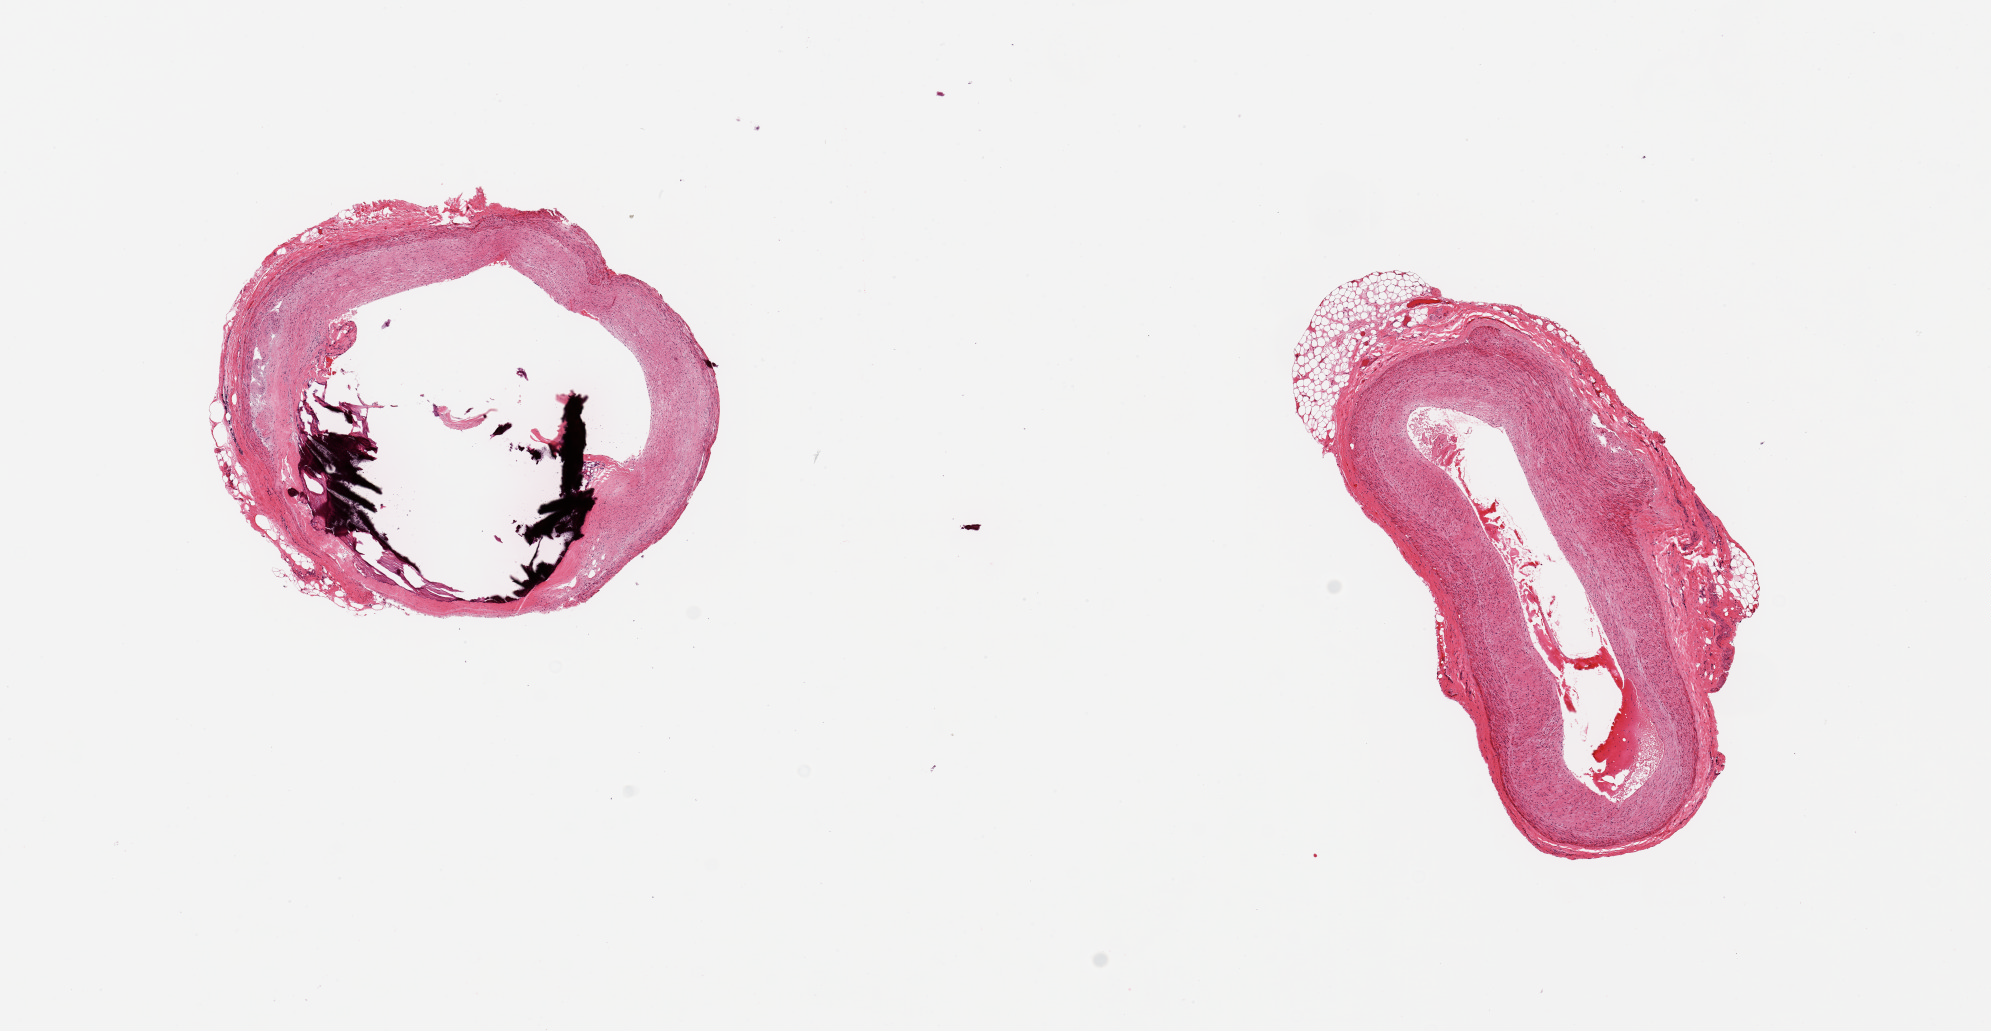
Digitized haematoxylin and eosin-stained section — whole scanned area (about 15.8 x 8.2 mm) shown as a low-resolution overview. PAXgene-fixed paraffin-embedded (PFPE) section. Section of coronary artery (target tissue). Donor tissue sample. Donor sex: male.
- pathologist's review note for this sample: 2 pieces; calcific atherosclerosis, 1.5mm attachment of fat and attachment of nerve on one piece